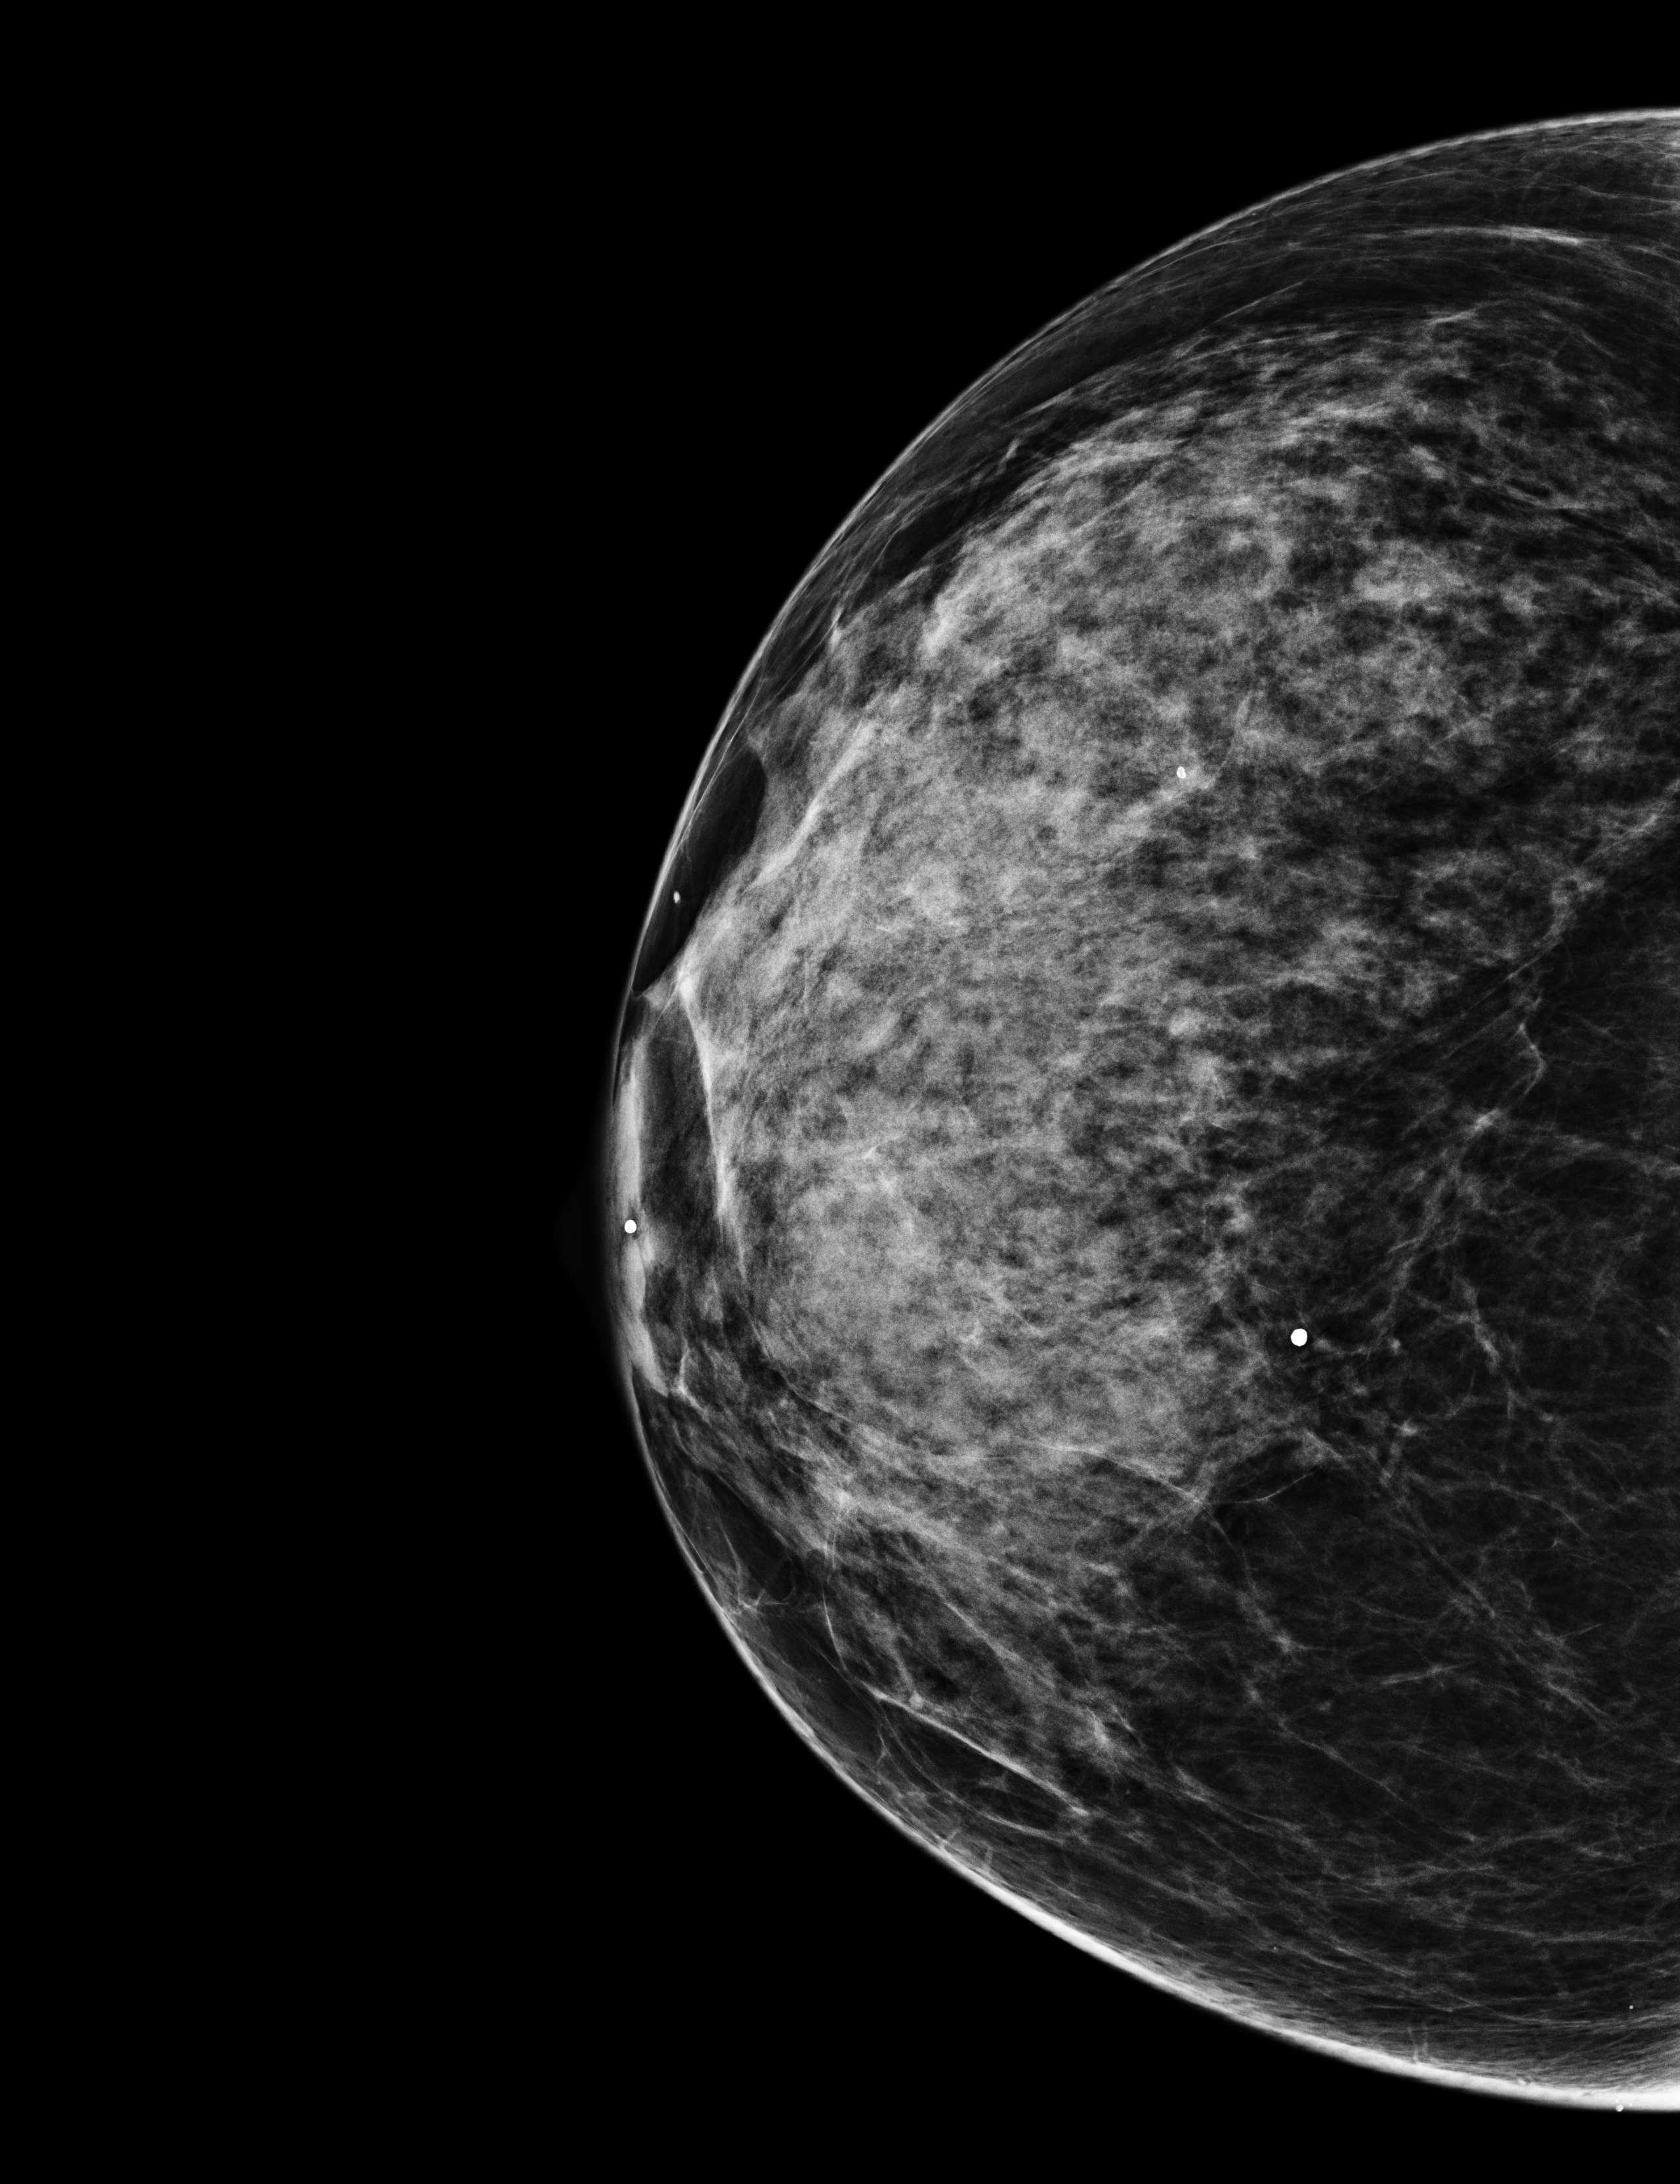
Annual screening mammography examination, system: Selenia Dimensions. Female patient, age 59 years.
Image type: full-field digital mammogram. Breast: right. Projection: CC view.